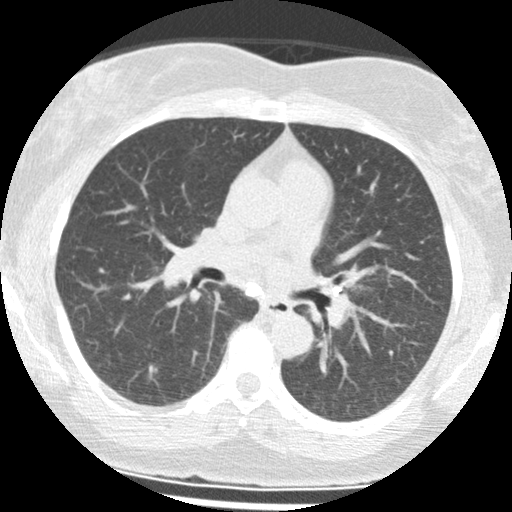
Axial slice from a low-dose chest CT screening exam, baseline screening round, lung window (W 1500 / L -600 HU), 2.5 mm slice thickness, standard (soft-tissue) reconstruction kernel (STANDARD). Female participant, aged 65 years at enrolment. Current smoker at enrolment.
Lesion marked by an expert reader, bounding box (x1, y1, x2, y2) in pixels: (132, 354, 170, 392). Screening reader's record for this exam (one nodule recorded; not confirmed to be the boxed lesion): non-calcified nodule or mass ≥4 mm, right lower lobe, 8 × 6 mm, poorly defined margins, mixed attenuation. Later outcome: lung cancer diagnosed 423 days after this screen — non-small cell carcinoma, right lower lobe, well differentiated (G1), stage IA (AJCC 6th edition), 10 mm at pathology.